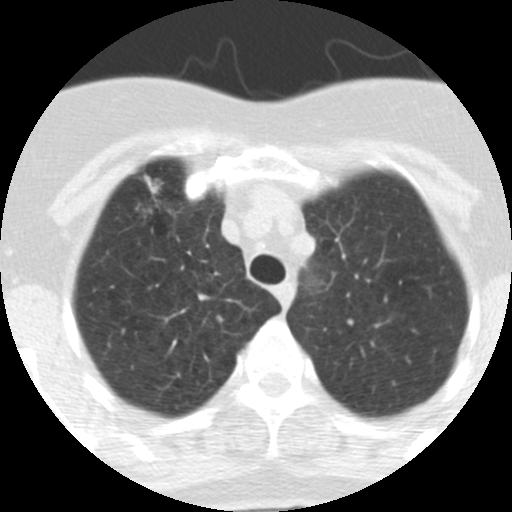
Low-dose screening chest CT, axial slice; baseline screening round; lung window (W 1500 / L -600 HU); standard (soft-tissue) reconstruction kernel (STANDARD); slice 60 of 313 in the series. Female participant, aged 62 years at enrolment.
- 2 expert reader's lesion annotations on this slice (largest first), bounding box [x1, y1, x2, y2] px = [116, 171, 190, 238]; [121, 167, 186, 223].
- Screening reader's record for this exam (one nodule recorded; not confirmed to be the boxed lesion): non-calcified nodule or mass ≥4 mm, right upper lobe, 9 × 7 mm, spiculated (stellate) margins, soft tissue attenuation.